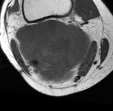
MRI of an extremity soft-tissue mass, one axial slice; position 28 of 45 along the scan axis; MR volume resampled by the dataset authors to the PET/CT grid (not the native acquisition matrix); 3.27 mm slice thickness; 113 × 111 image matrix, field of view 110 × 108 mm. Female patient. From the clinical record (not read from this slice): histological type: liposarcoma; site of the primary tumour: right thigh.
Outlined on this slice (expert contour drawn on MRI and transferred to this co-registered scan by the dataset authors):
- gross tumour volume (mass): bounding box (x1, y1, x2, y2) in pixels: (15, 19, 93, 84)